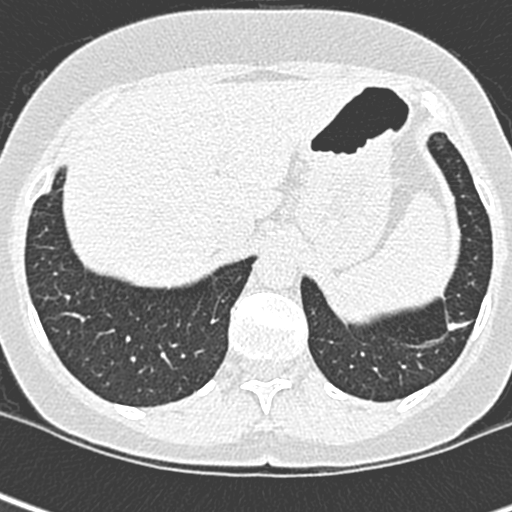
Low-dose screening chest CT, one axial slice. Position 52 of 252 along the scan axis. Lung window (W 1500 / L -600 HU). 1.3 mm slice thickness. 512 × 512 image matrix, field of view 271 × 271 mm.
Annotated regions visible in this slice (manually delineated by an expert):
- lesion 1 (tumor, lower lobe of left lung): bounding box <447,313,472,331> (left, top, right, bottom; pixels)